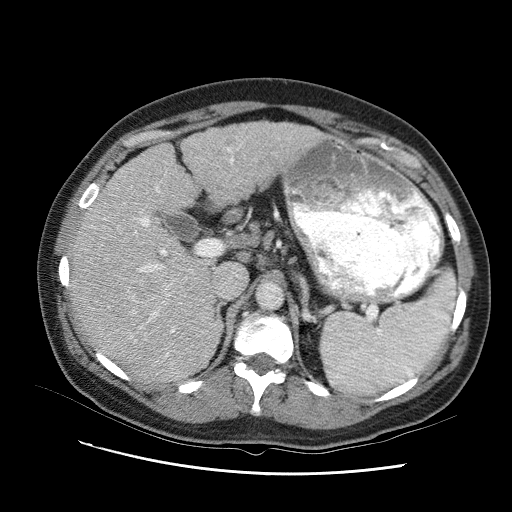
Contrast-enhanced abdominal CT (liver protocol), one axial slice. Position 60 of 95 along the scan axis. Reconstruction kernel STANDARD. 120 kVp. One of 2 acquisitions stored at this slice position. Soft-tissue window (W 400 / L 40 HU). 2.5 mm slice thickness. 512 × 512 image matrix. Case-level facts recorded for this patient, not image findings: diagnosis: hepatocellular carcinoma (patient treated with transarterial chemoembolisation; whether this scan precedes or follows treatment is not stated here); TNM stage (as recorded): Stage-I.
Structures marked on this image (semi-automatic segmentation, software-assisted and operator-edited):
- abdominal aorta: box from (x=256, y=282) to (x=281, y=308) px
- liver parenchyma outside the tumour (the mass and vessels are separate outlines, so this box may not span the whole liver): (x=68, y=117)–(x=326, y=378)
- liver vessels: (x=94, y=131)–(x=325, y=347)